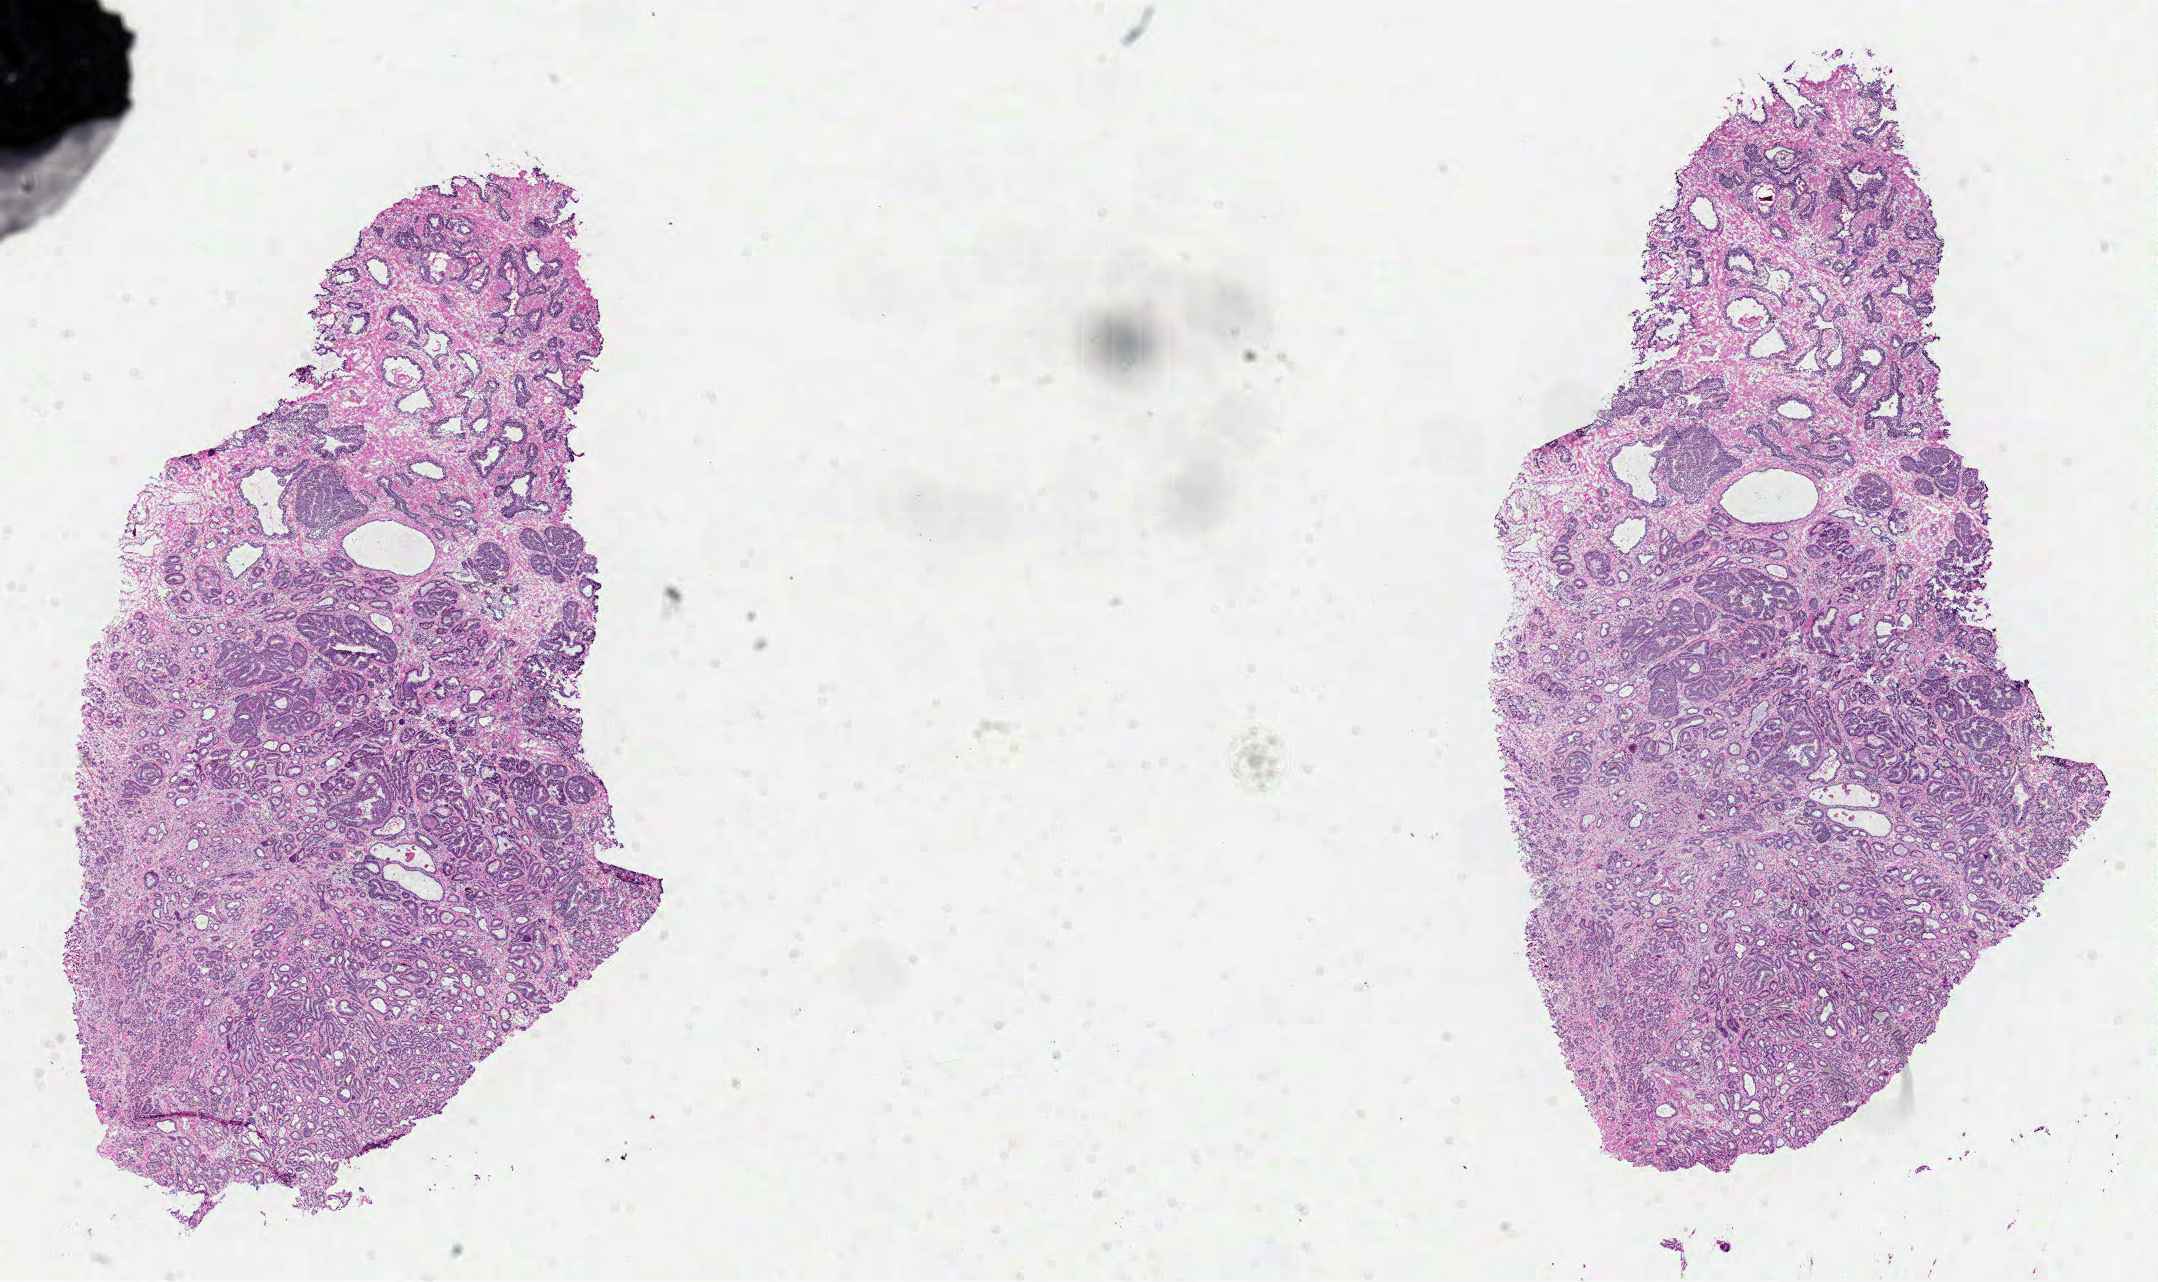
Digitized H&E tissue section (whole slide), whole scanned area (about 17.4 x 10.3 mm) shown as a low-resolution overview, formalin-fixed paraffin-embedded (FFPE) diagnostic section, primary tumour sample from the prostate. Patient: male, age at initial diagnosis 66 years. Gleason score: 7 (3+4).
Lymph nodes positive (case pathology): 0 of 1 examined. Diagnosis: Acinar cell carcinoma (prostate gland). Laterality: bilateral.